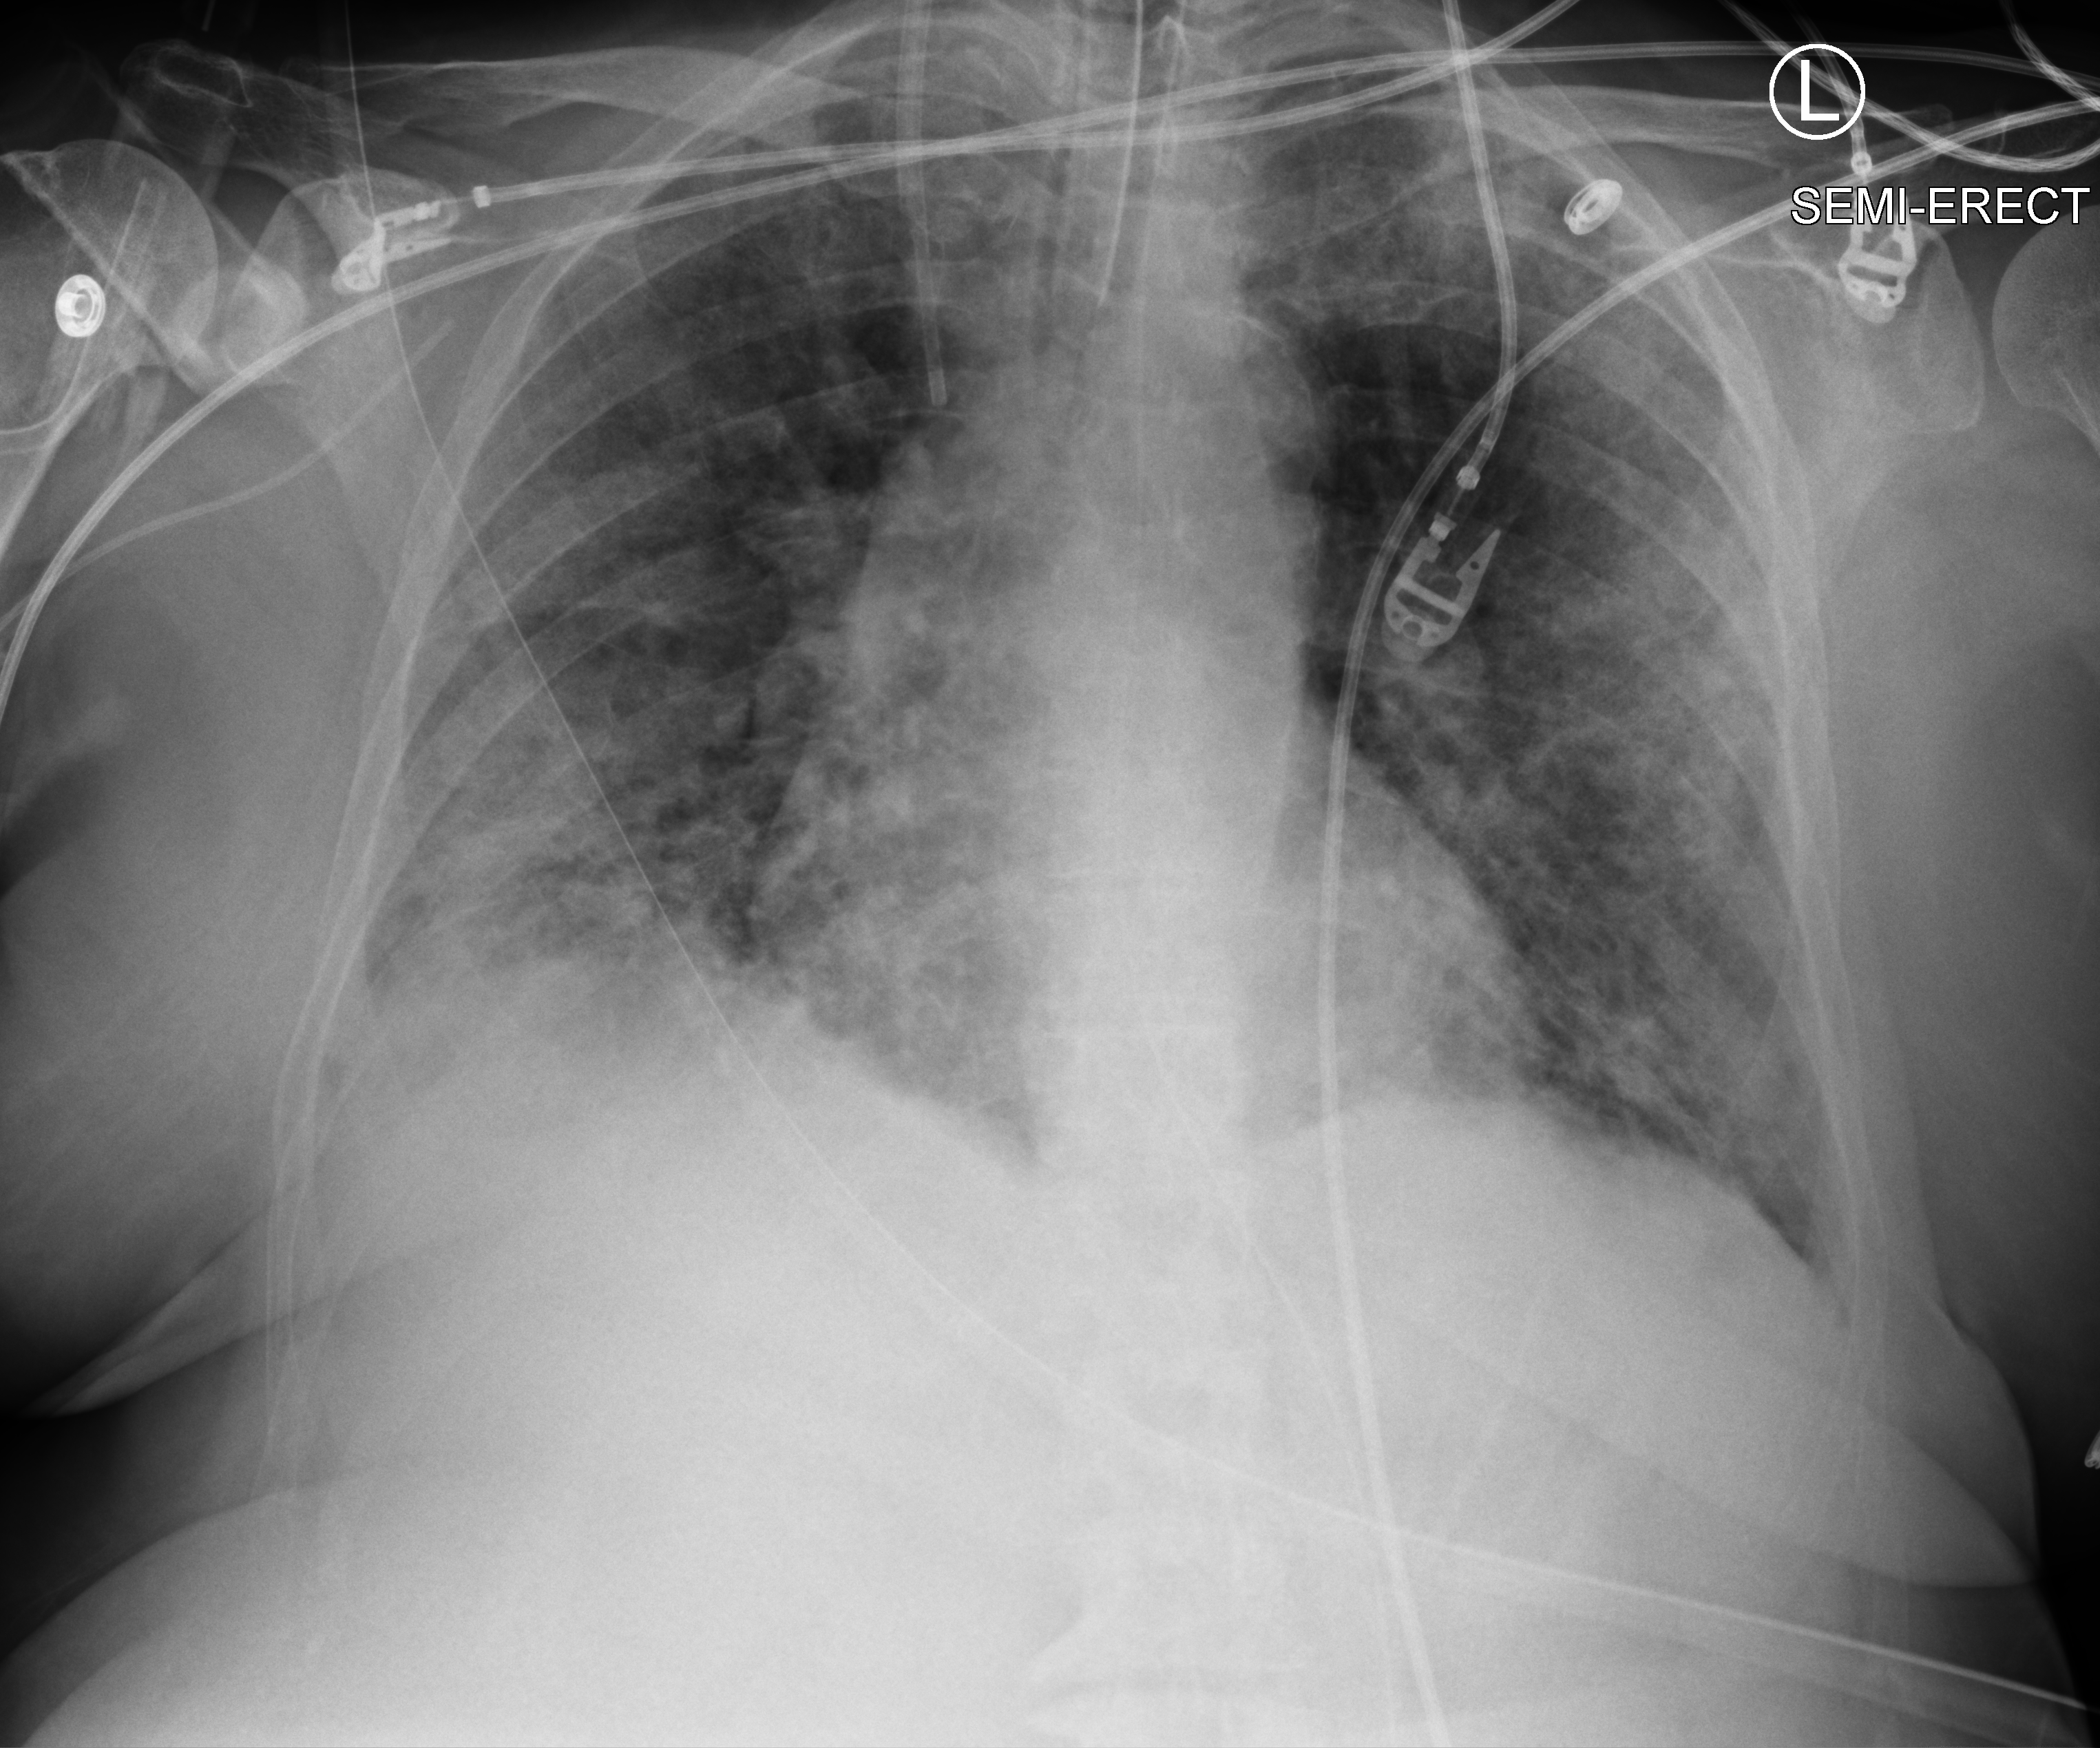
Bedside chest radiograph (computed radiography), anteroposterior (AP) projection. Patient hospitalised with COVID-19; female, aged 75–90 years.
Admission-level facts for this patient (not findings on this image; timing relative to this image not recorded): diabetes (admission record): no; mechanically ventilated during this hospital stay: yes.